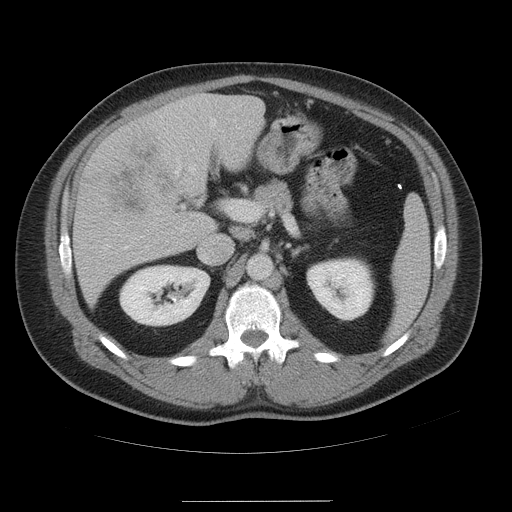
Contrast-enhanced abdominal CT, one axial slice; slice 28 of 54 in the series (ordered by position); 120 kVp; intravenous contrast given; soft-tissue window (W 400 / L 40 HU); 5 mm slice thickness; 512 × 512 image matrix, field of view 436 × 436 mm. Male patient, age 40 years. Case-level facts recorded for this patient, not image findings: diagnosis: colorectal cancer liver metastases, imaged before liver resection; multiple liver metastases: no.
Annotated regions visible in this slice (manually delineated by an expert):
- liver: box from (x=73, y=94) to (x=265, y=309) px
- planned liver remnant (the part of the liver to remain after resection): (x=212, y=96)–(x=265, y=170)
- liver metastasis: (x=82, y=122)–(x=181, y=220)